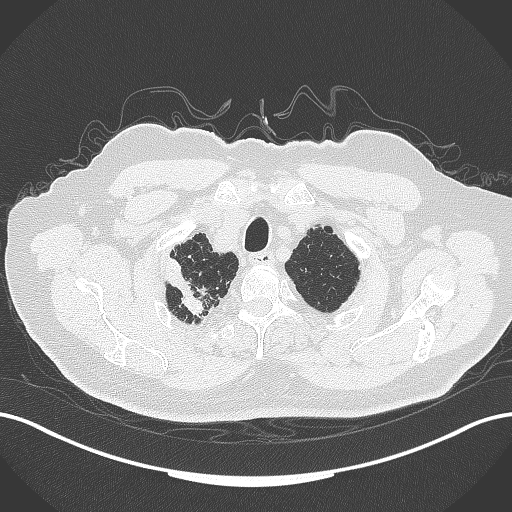
Chest CT, one axial slice. Slice 325 of 389 in the series (ordered by position). Reconstruction kernel B70f. Lung window (W 1500 / L -600 HU). 1 mm slice thickness. 512 × 512 image matrix, field of view 400 × 400 mm. Male patient, age 72 years. From the clinical record (not read from this slice): clinical TNM (as recorded): T1a N0 M0.
Annotated regions visible in this slice (rectangle marked by the reading radiologist):
- lung tumour (recorded histology: squamous cell carcinoma): bounding box (x1, y1, x2, y2) in pixels: (162, 253, 208, 316)